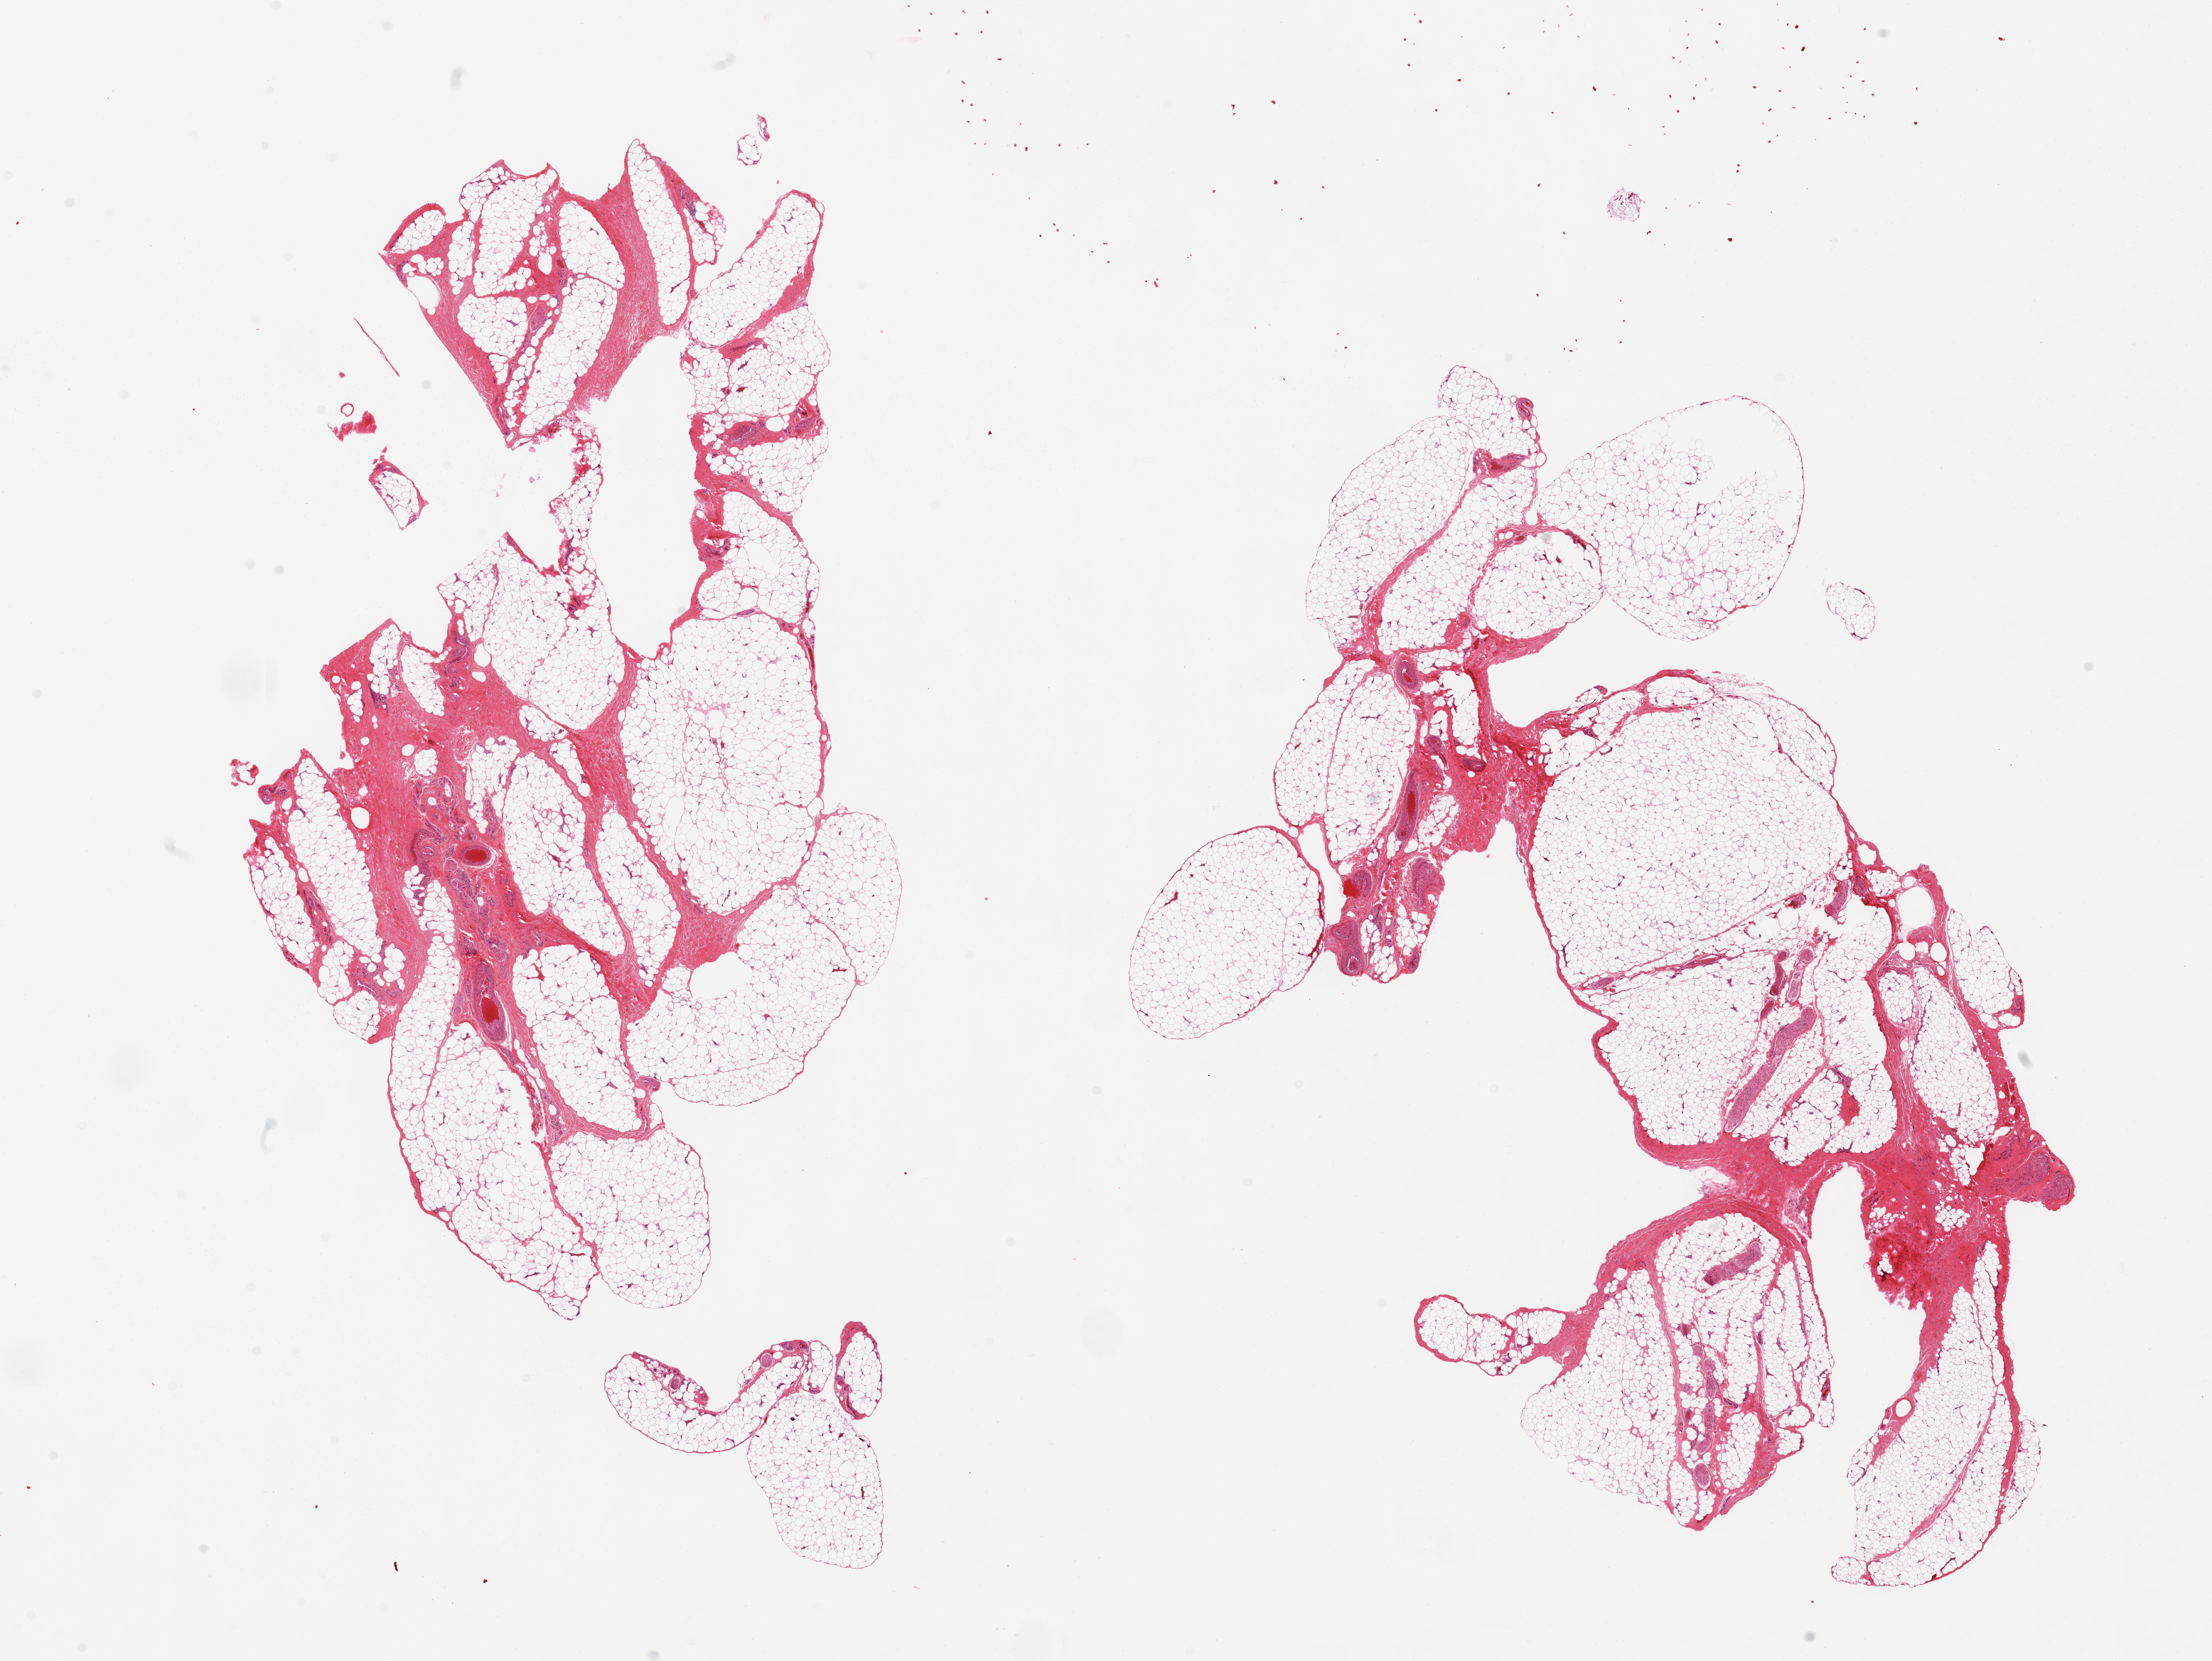
Whole-slide image, hematoxylin and eosin (H&E) stain — whole scanned area (about 24.6 x 18.5 mm, acquisition: 20x scan) shown as a low-resolution overview, PAXgene-fixed, paraffin-embedded tissue, section of adipose tissue (target tissue), tissue donor sample. Donor: male.
• pathologist's review note for this sample: 2 pieces, ~30-40% fibro-fascial elements